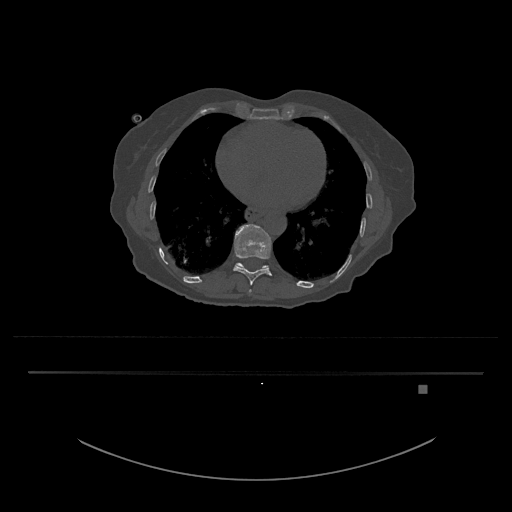
CT including the spine, one axial slice. Position 705 of 797 along the scan axis. Reconstruction kernel Br40s/3. Bone window (W 1800 / L 400 HU). 0.5 mm slice thickness. 512 × 512 image matrix. Female patient, age 57 years. Case-level facts recorded for this patient, not image findings: primary cancer: cervical.
Structures marked on this image (semi-automatic segmentation, software-assisted and operator-edited):
- T10 vertebra: bounding box (x1, y1, x2, y2) in pixels: (233, 224, 272, 286)
- T11 vertebra: (236, 263, 269, 270)
- T9 vertebra: (249, 289, 252, 293)